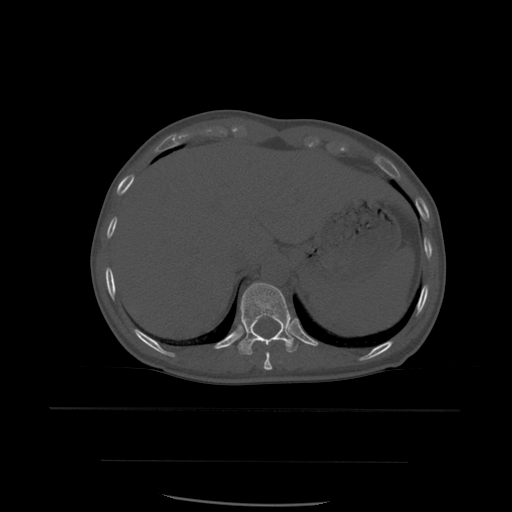
CT including the spine, one axial slice. Slice 299 of 574 in the series (ordered by position). Bone window (W 1800 / L 400 HU). 1.25 mm slice thickness. 512 × 512 image matrix, field of view 392 × 392 mm. Patient age 48 years. From the clinical record (not read from this slice): primary cancer: lung.
Outlined on this slice (semi-automatically segmented with operator editing):
- T10 vertebra: bounding box <264,341,288,371> (left, top, right, bottom; pixels)
- T11 vertebra: <238,283,299,355>